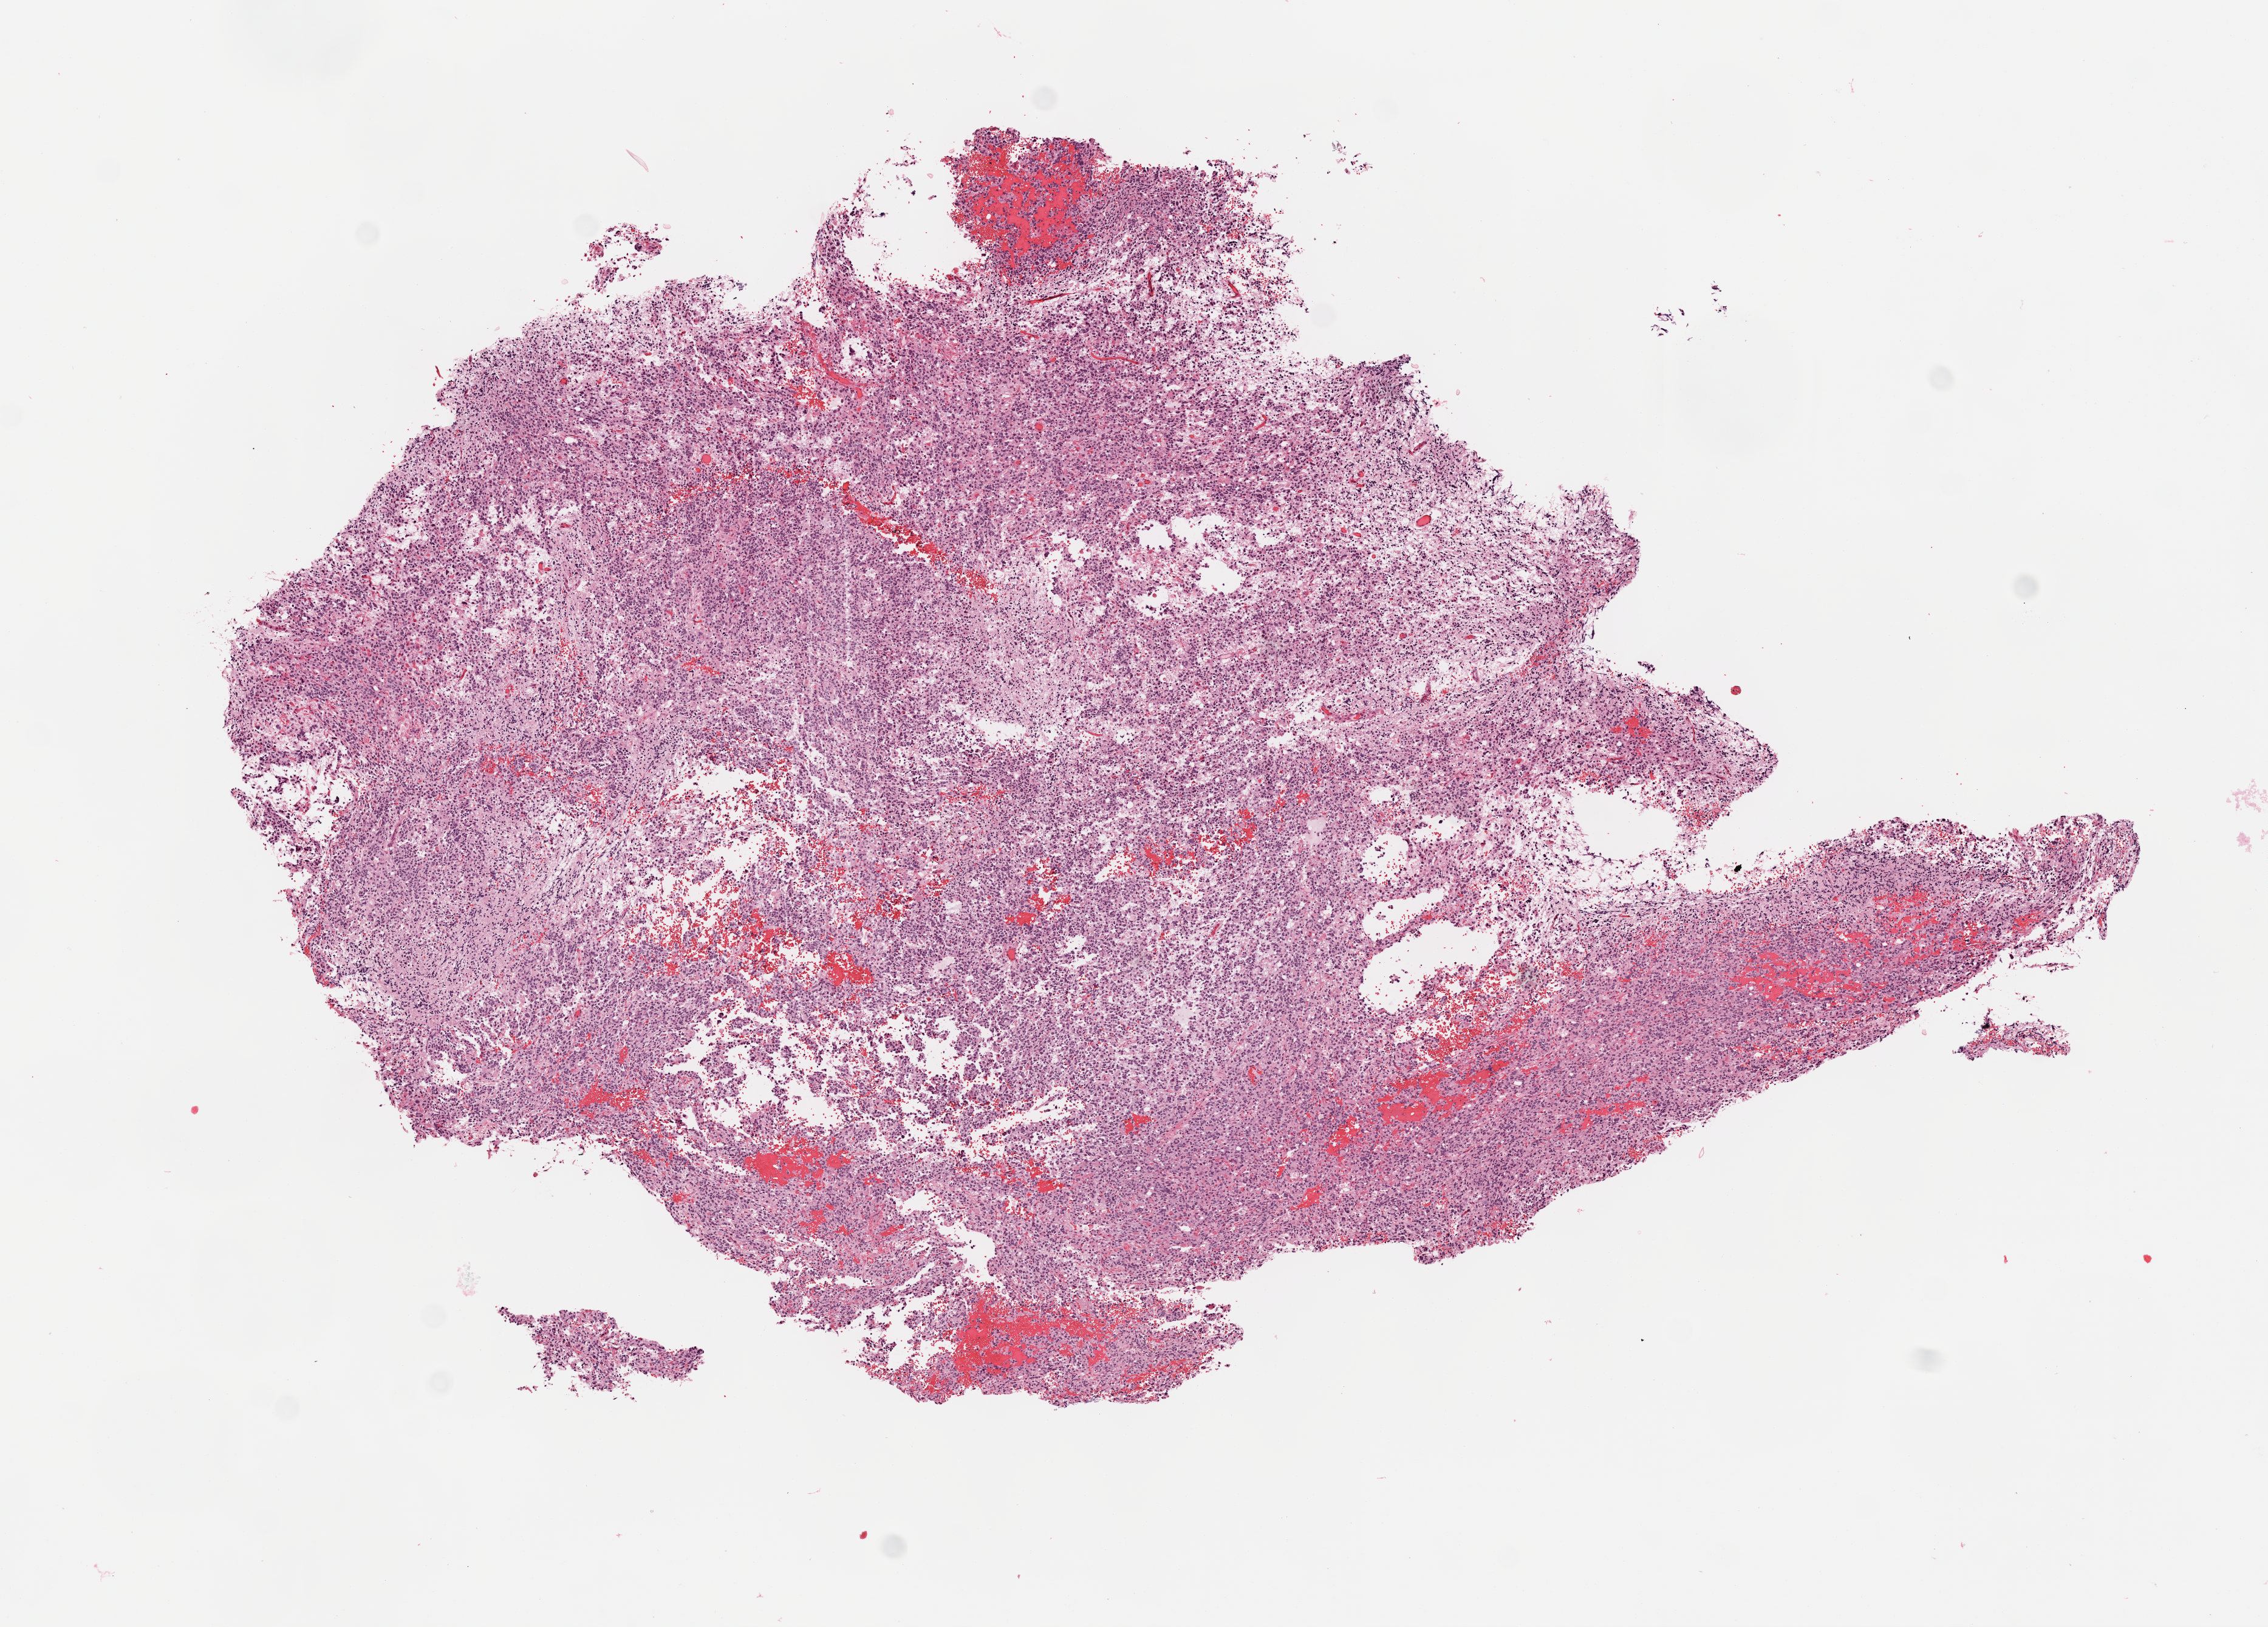
Whole-slide histology image, H&E — low-resolution overview of the scanned area, about 7.6 x 5.4 mm. FFPE section. Primary tumour sample from the brain. Female, age 54 years at initial diagnosis. Histologic grade: G3 (poorly differentiated).
• pathologic diagnosis: Astrocytoma, anaplastic